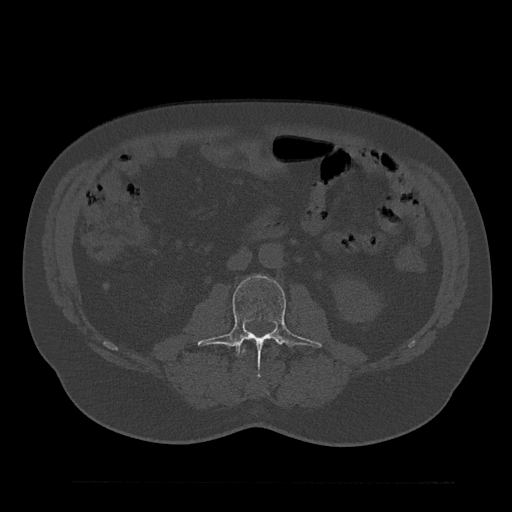
CT including the spine, one axial slice. Position 41 of 797 along the scan axis. Reconstruction kernel Br40s/3. 120 kVp. Bone window (W 1800 / L 400 HU). 0.5 mm slice thickness. 512 × 512 image matrix, field of view 430 × 430 mm. Male patient, age 61 years. From the clinical record (not read from this slice): primary cancer: prostate.
Annotated regions visible in this slice (semi-automatic segmentation, software-assisted and operator-edited):
- L2 vertebra: bounding box [x1, y1, x2, y2] px = [241, 348, 275, 354]
- L3 vertebra: [197, 275, 323, 362]